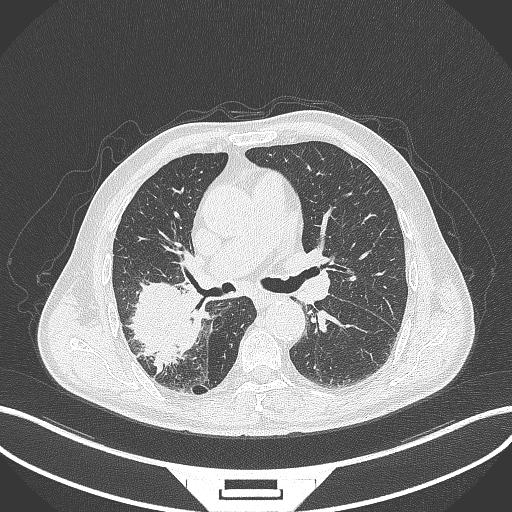
Chest CT, one axial slice; position 239 of 429 along the scan axis; 120 kVp; lung window (W 1500 / L -600 HU); 512 × 512 image matrix, field of view 400 × 400 mm. Male patient, age 72 years. Case-level facts recorded for this patient, not image findings: clinical TNM (as recorded): T3 N2 M0.
Structures marked on this image (bounding box drawn by a radiologist):
- lung tumour (recorded histology: adenocarcinoma): bounding box (x1, y1, x2, y2) in pixels: (127, 274, 203, 370)